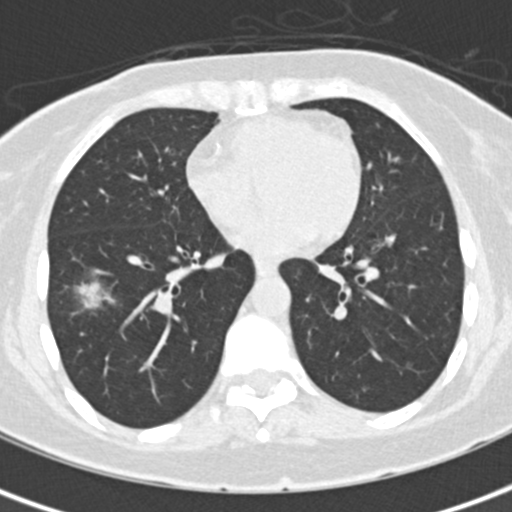
Low-dose screening chest CT, axial slice; baseline screening round; lung window (W 1500 / L -600 HU); 2 mm slice thickness; 120 kVp; slice 100 of 171 in the series; 512 × 512 image matrix. Female participant, aged 56 years at enrolment. Former smoker at enrolment.
• Expert reader's lesion annotation, bounding box (x1, y1, x2, y2) in pixels: (63, 270, 127, 326).
• The screening reader recorded 5 non-calcified nodules or masses ≥4 mm on this exam (right lower lobe, right upper lobe, left upper lobe, left lower lobe, left lower lobe); which of them this box marks is not recorded.